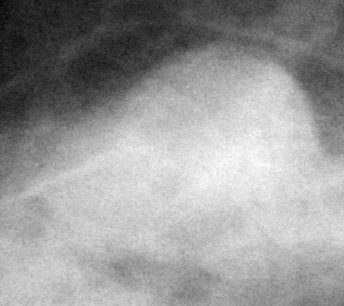
Cropped region of a digitized screen-film mammogram centred on a radiologist-marked abnormality; right breast; CC view; BI-RADS breast density category 2 (scale 1–4).
Finding: mass, shape oval, margins circumscribed; BI-RADS assessment category 4; subtlety rating 5 on a 1 (subtle) to 5 (obvious) scale; pathology (as recorded): benign.